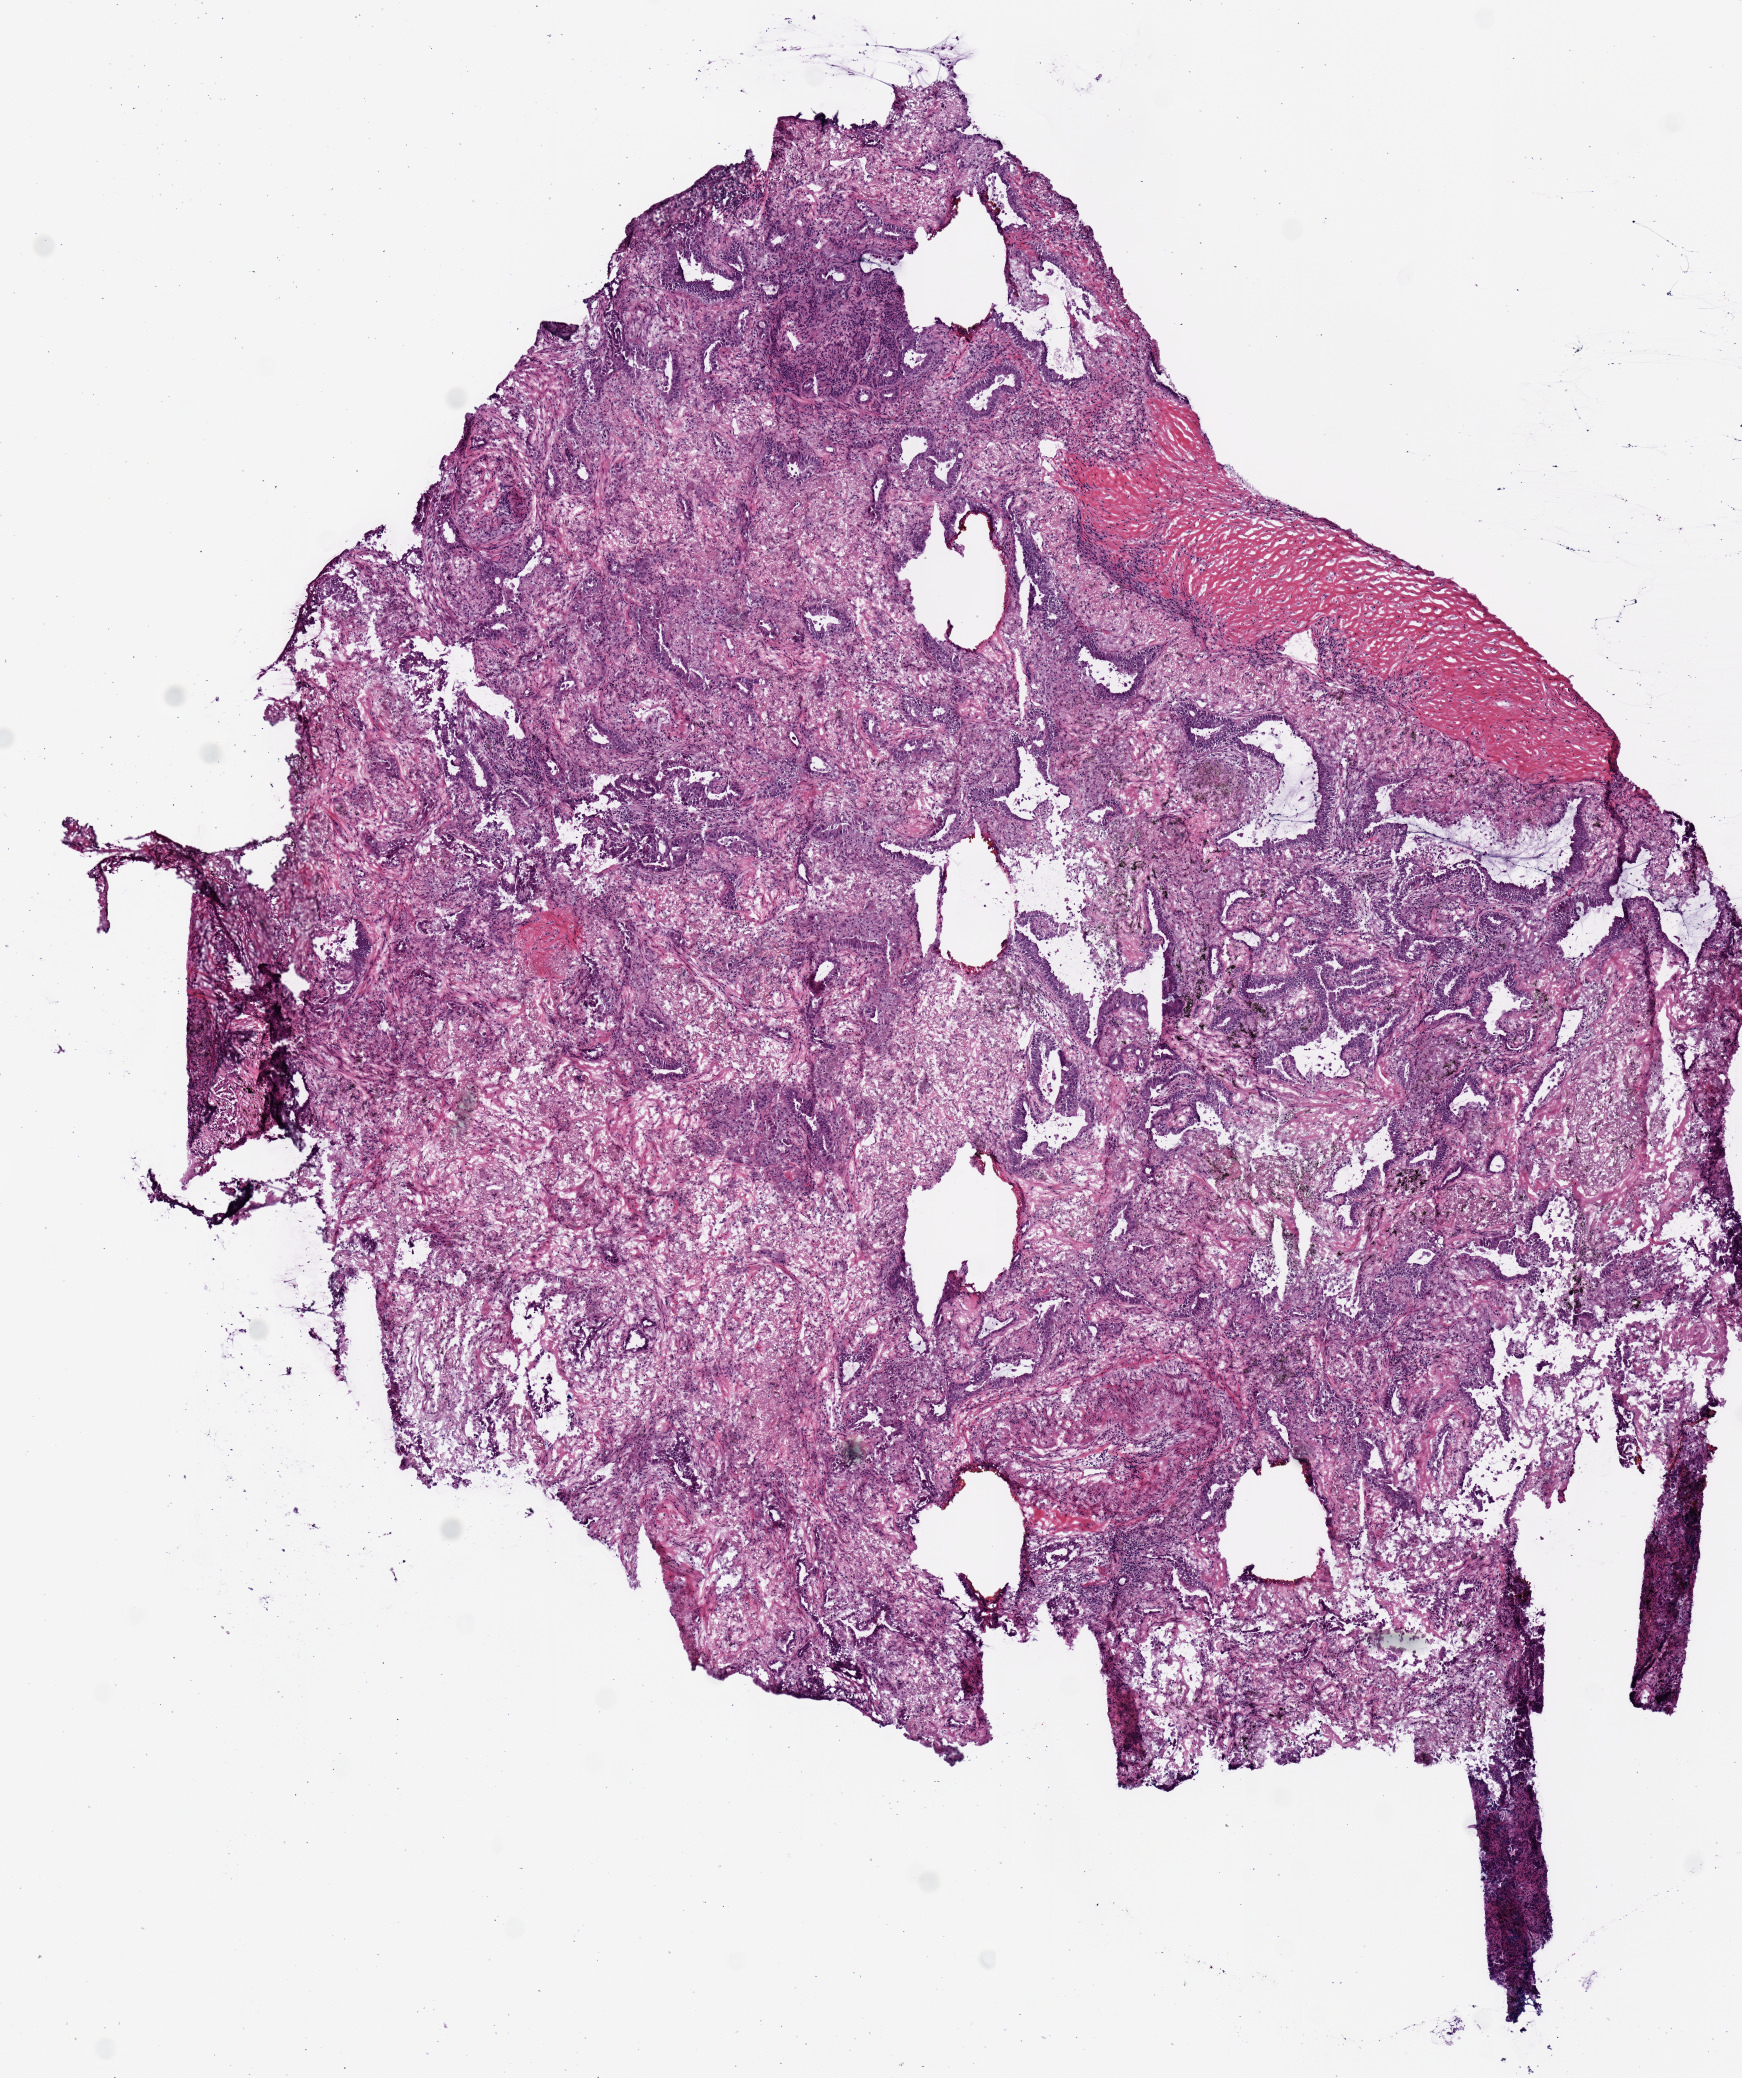
H&E whole-slide image, shown as a low-resolution overview of the whole scanned area (about 6.9 x 8.2 mm); frozen section; sample: primary tumour, lung. Female patient; age at initial diagnosis 67 years. Slide review estimates, as recorded: tumour cells 55%, tumour nuclei 65%, normal cells 0%, stromal cells 40%, necrosis 5%.
- AJCC pathologic stage: IB
- diagnosis: Adenocarcinoma, NOS